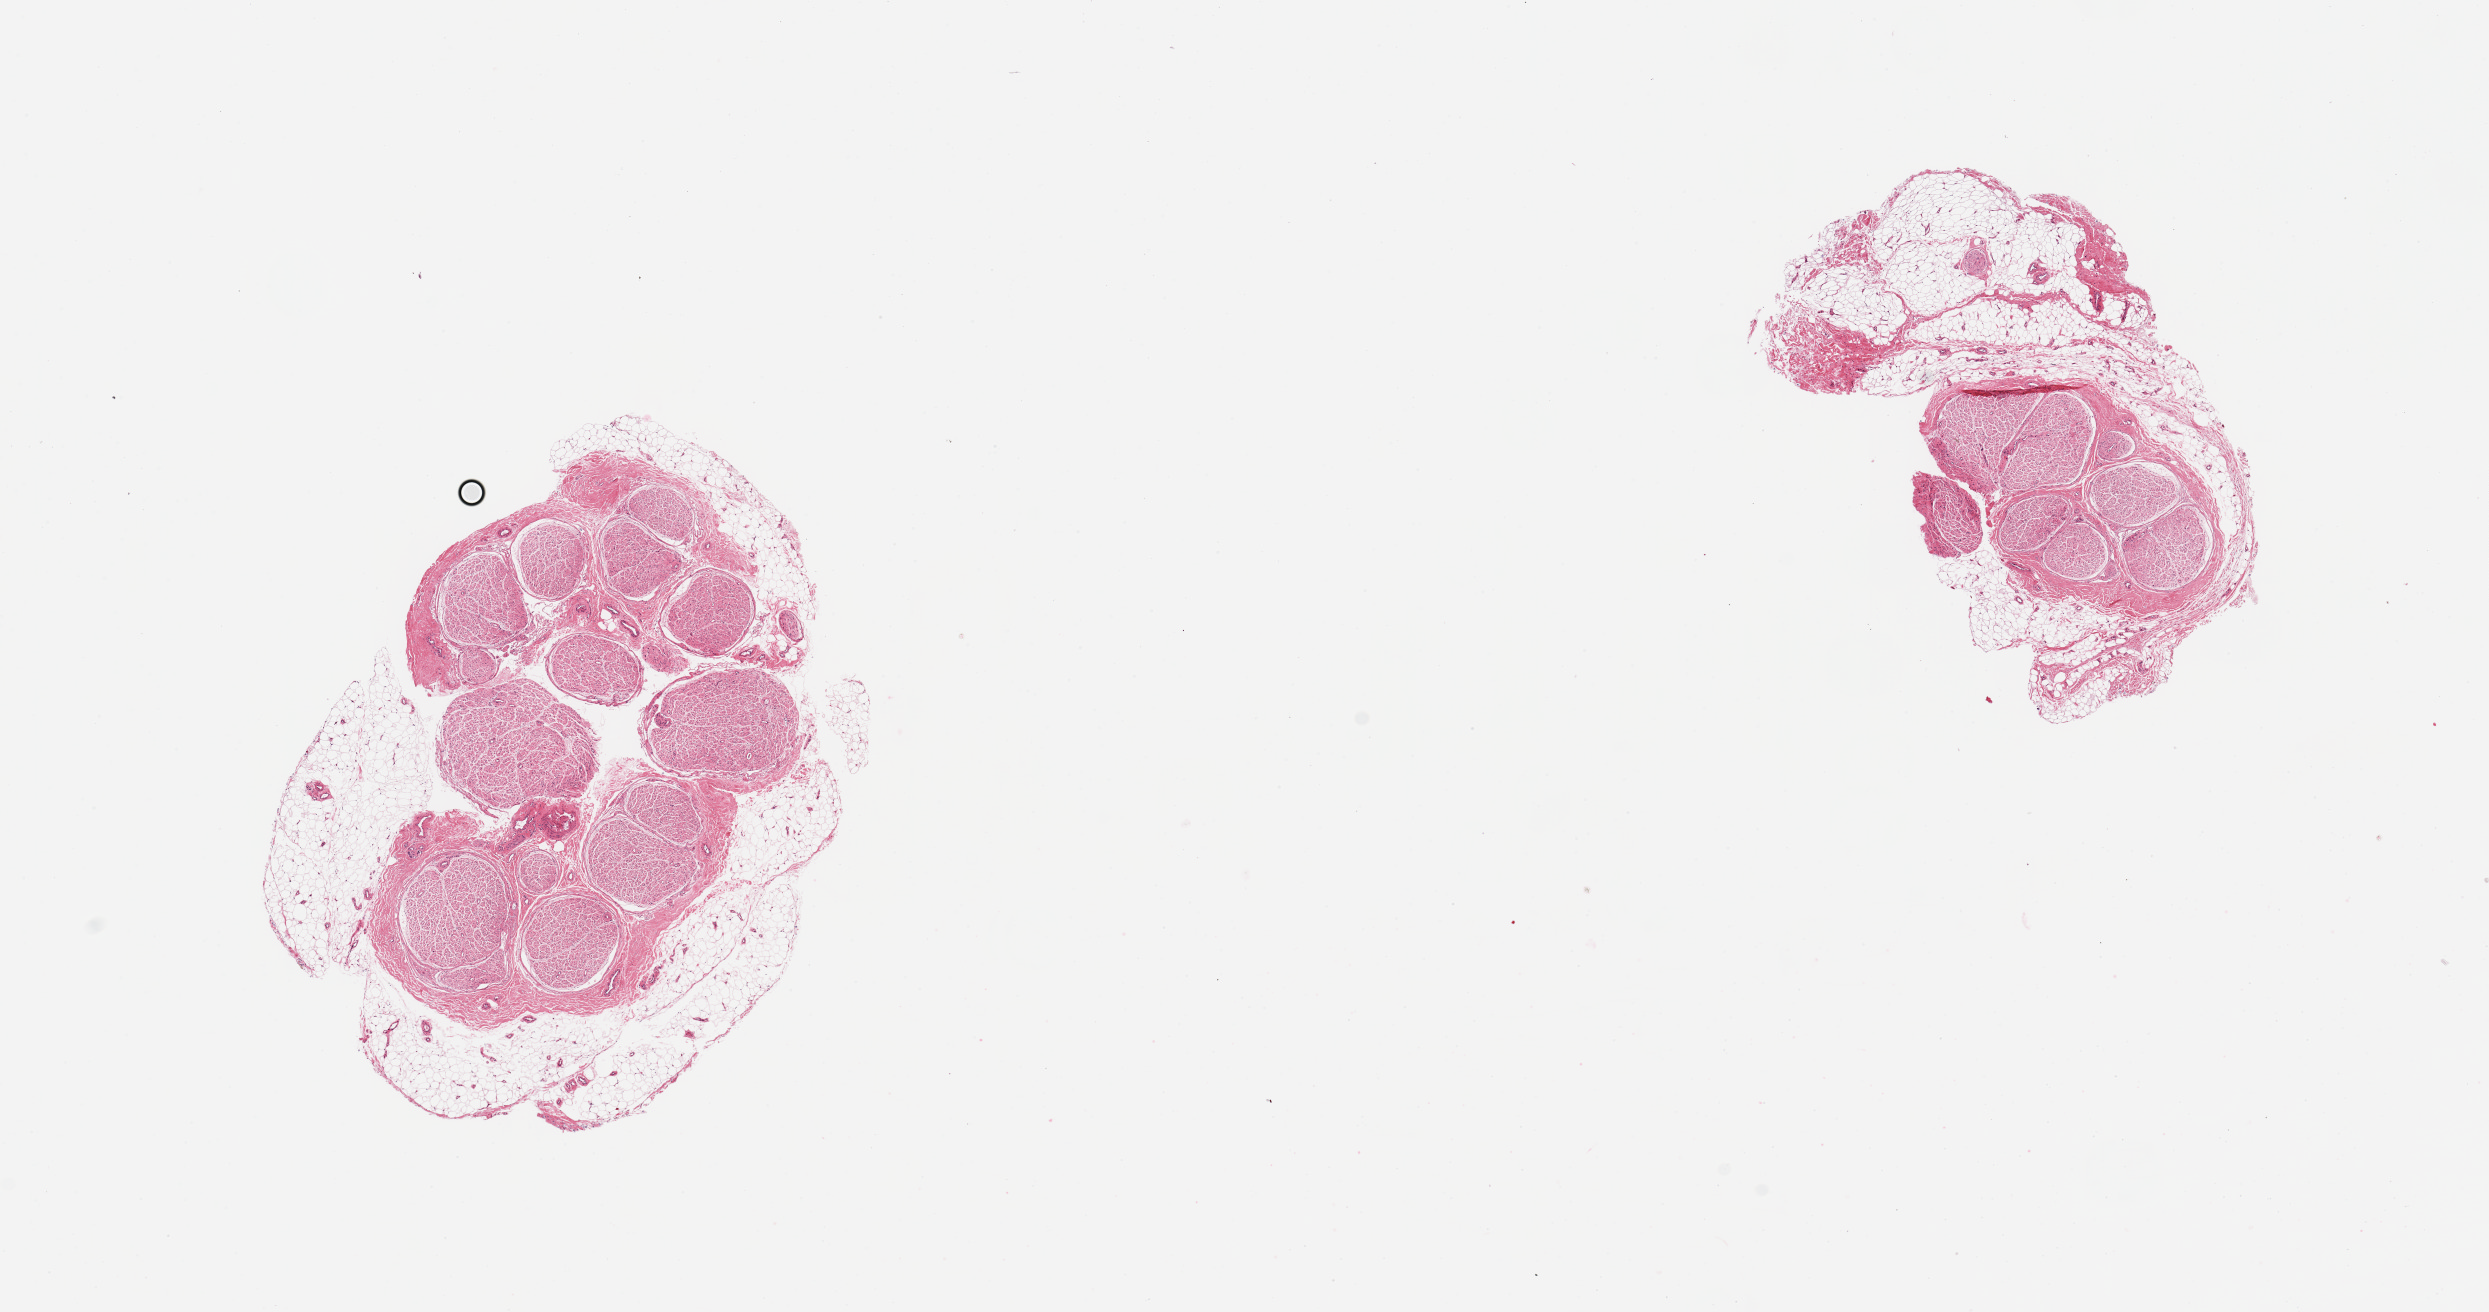
Digitized hematoxylin and eosin (H&E)-stained section, a low-resolution overview of the entire scanned area, about 19.7 x 10.4 mm (from a 20x scan). PAXgene-fixed paraffin-embedded (PFPE) section. Sampled site (target tissue): tibial nerve. Tissue donor sample. Donor sex: male.
Pathologist's review note for this sample: 2 pieces, rim of adherent fat up to ~2mm.